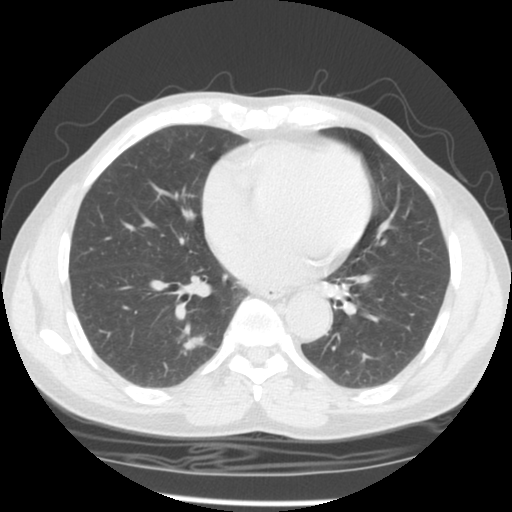
Axial slice from a low-dose chest CT screening exam. Third annual screen. Lung window (W 1500 / L -600 HU). 2.5 mm slice thickness. Slice 57 of 127 in the series. Male participant, aged 58 years at enrolment. Current smoker at enrolment.
Lesion marked by an expert reader, bounding box <167,327,216,362> (left, top, right, bottom; pixels). The screening reader recorded 2 non-calcified nodules or masses ≥4 mm on this exam (left upper lobe, right lower lobe); which of them this box marks is not recorded. Official screen result: positive, other. Lung cancer was diagnosed 323 days after this screen: adenocarcinoma, NOS, right lower lobe, poorly differentiated (G3), stage IIIA (AJCC 6th edition), 15 mm at pathology.